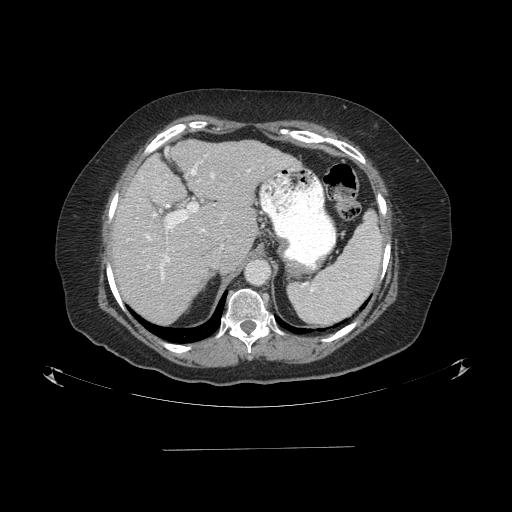
Contrast-enhanced abdominal CT (liver protocol), one axial slice; slice 60 of 103 in the series (ordered by position); reconstruction kernel STANDARD; one of 2 acquisitions stored at this slice position; soft-tissue window (W 400 / L 40 HU); 2.5 mm slice thickness; 512 × 512 image matrix, field of view 500 × 500 mm. From the clinical record (not read from this slice): diagnosis: hepatocellular carcinoma (patient treated with transarterial chemoembolisation; whether this scan precedes or follows treatment is not stated here); TNM stage (as recorded): Stage-IIIA; Child-Pugh class: A; tumour differentiation: poorly differentiated; tumour nodularity: multinodular.
Outlined on this slice (semi-automatic segmentation, software-assisted and operator-edited):
- abdominal aorta: bounding box (x1, y1, x2, y2) in pixels: (247, 261, 269, 284)
- liver parenchyma outside the tumour (the mass and vessels are separate outlines, so this box may not span the whole liver): (112, 140, 300, 322)
- liver vessels: (127, 165, 249, 280)